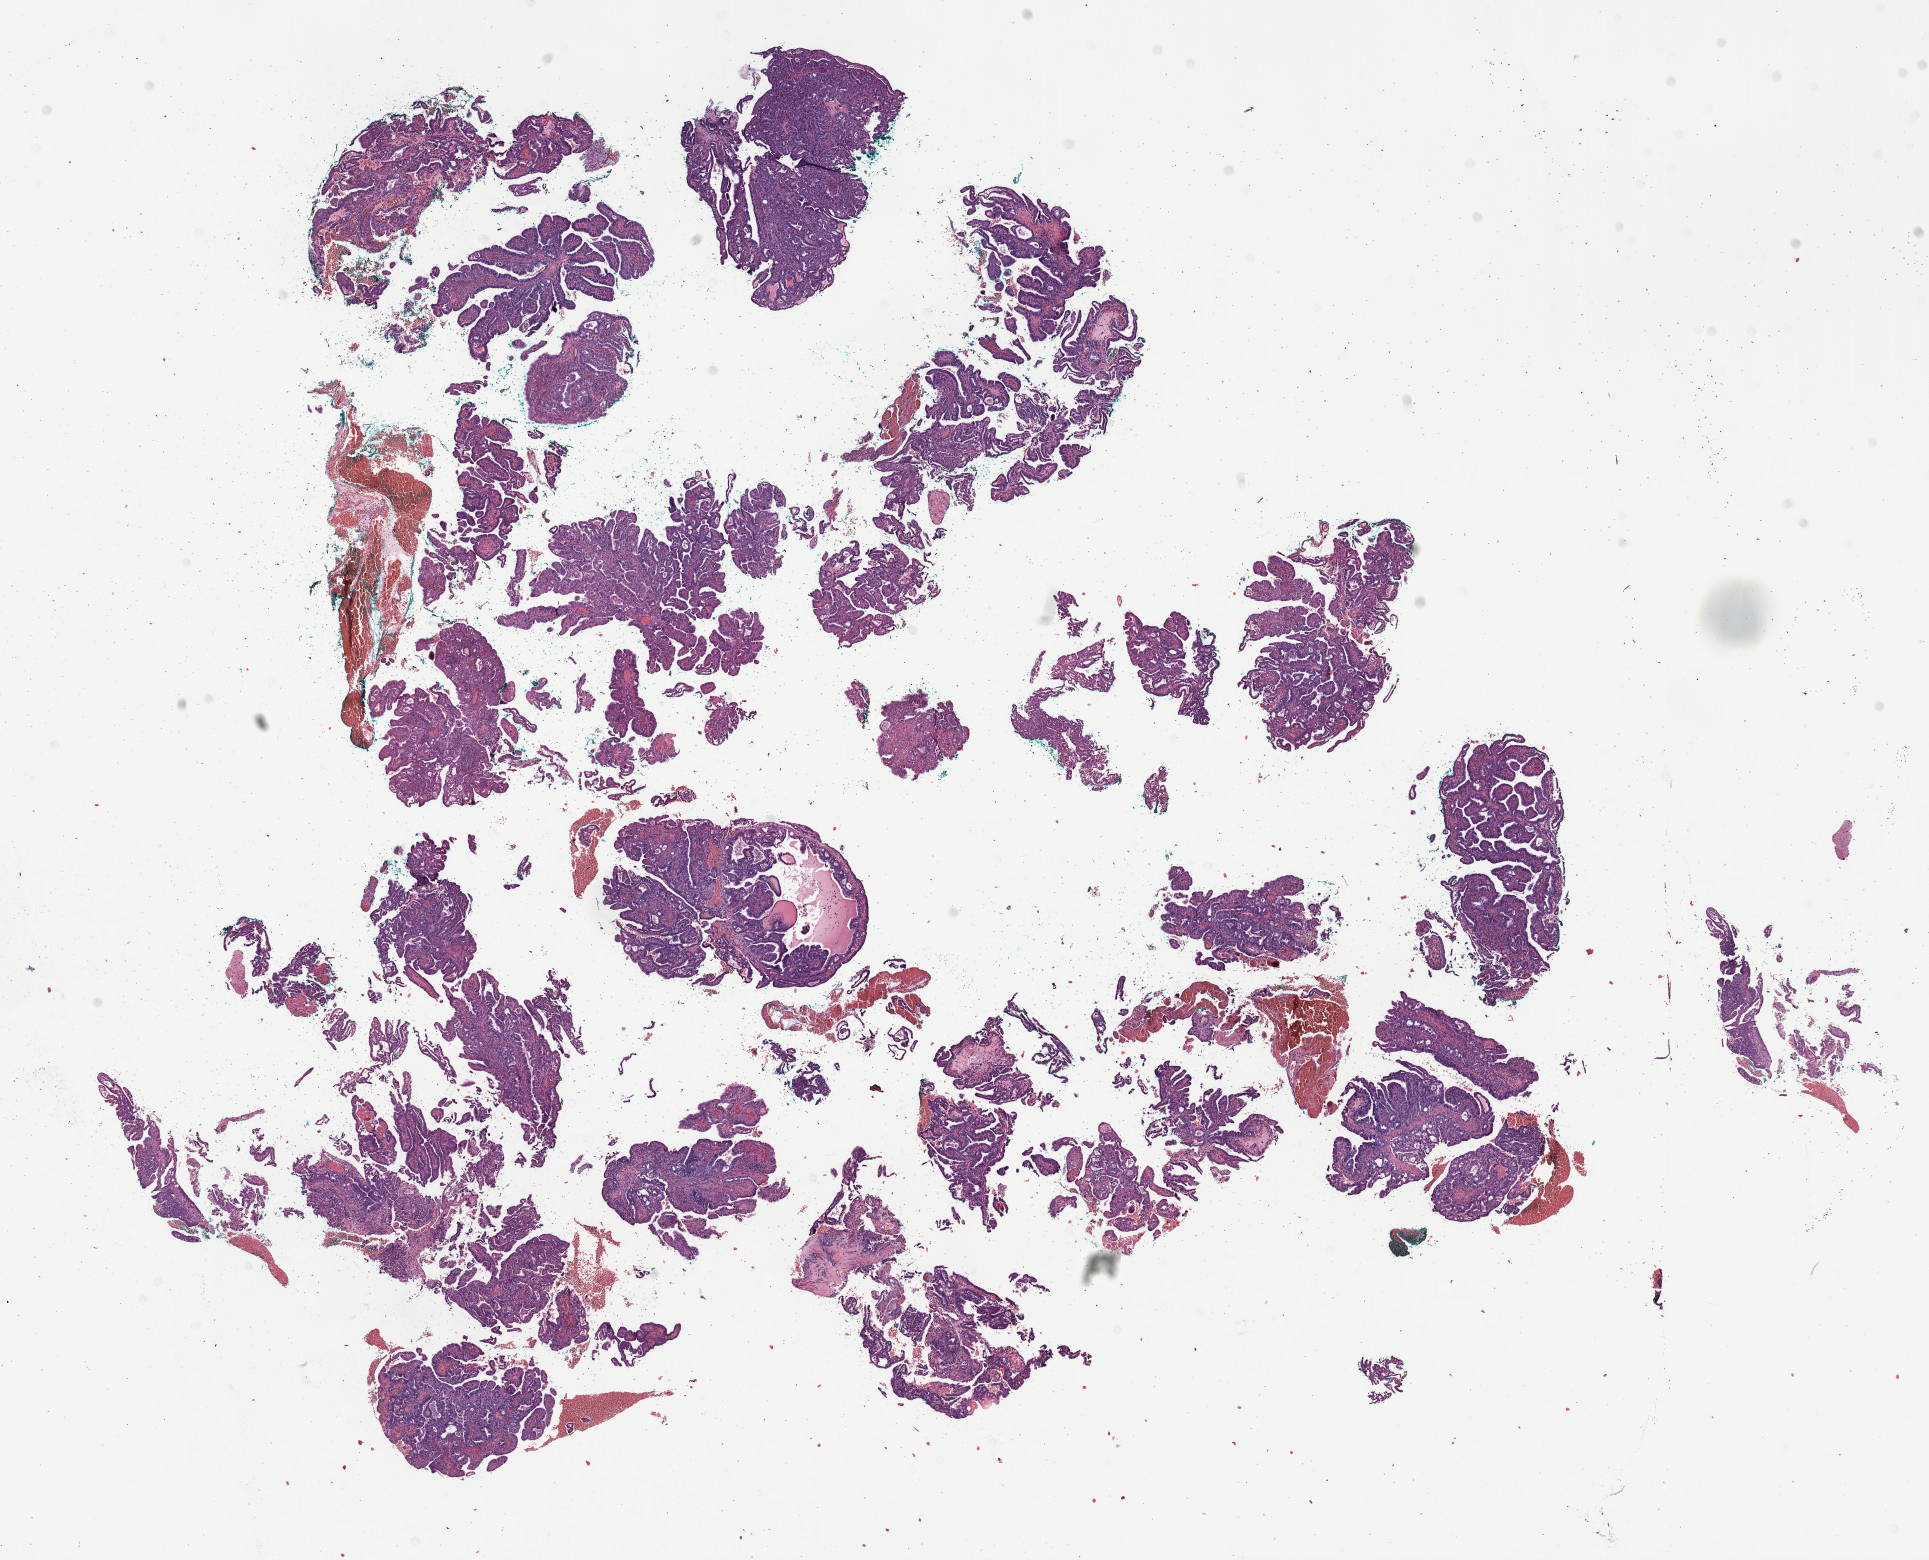
Digitized Hematoxylin and eosin (H&E) stained tissue section (whole slide), whole scanned area (about 15.6 x 12.6 mm) shown as a low-resolution overview, FFPE section, primary tumour sample from the cervix. Female, age 58 years at initial diagnosis. Histologic grade: G3 (poorly differentiated).
- pathologic diagnosis: Mucinous adenocarcinoma, endocervical type (cervix uteri)
- FIGO stage: IB